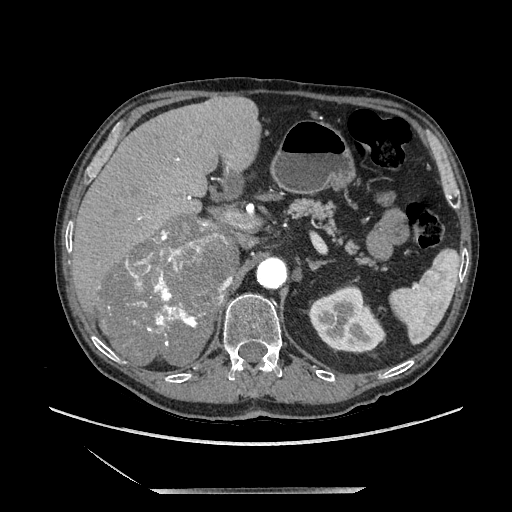
Contrast-enhanced abdominal CT, one axial slice. Slice 132 of 243 in the series (ordered by position). Soft-tissue window (W 400 / L 40 HU). 512 × 512 image matrix, field of view 420 × 420 mm. Male patient. From the clinical record (not read from this slice): diagnosis: adrenocortical carcinoma; tumour side: right adrenal; tumour size at pathology: 16 cm; Ki-67 index: 17 %; stage (as recorded): 3.
Structures marked on this image (semi-automatic segmentation, software-assisted and operator-edited):
- mass: bounding box [x1, y1, x2, y2] px = [102, 218, 236, 364]